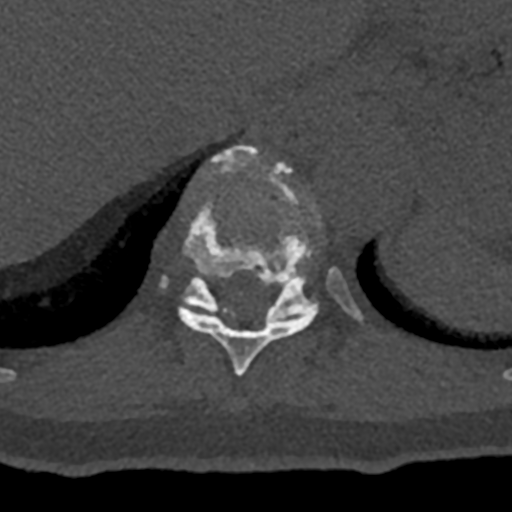
CT including the spine, one axial slice. Position 584 of 797 along the scan axis. 120 kVp. Bone window (W 1800 / L 400 HU). 0.5 mm slice thickness. 512 × 512 image matrix. Male patient, age 74 years. Case-level facts recorded for this patient, not image findings: primary cancer: renal.
Annotated regions visible in this slice (semi-automatically segmented with operator editing):
- T10 vertebra: bounding box <178,146,316,376> (left, top, right, bottom; pixels)
- T11 vertebra: <160,163,363,321>